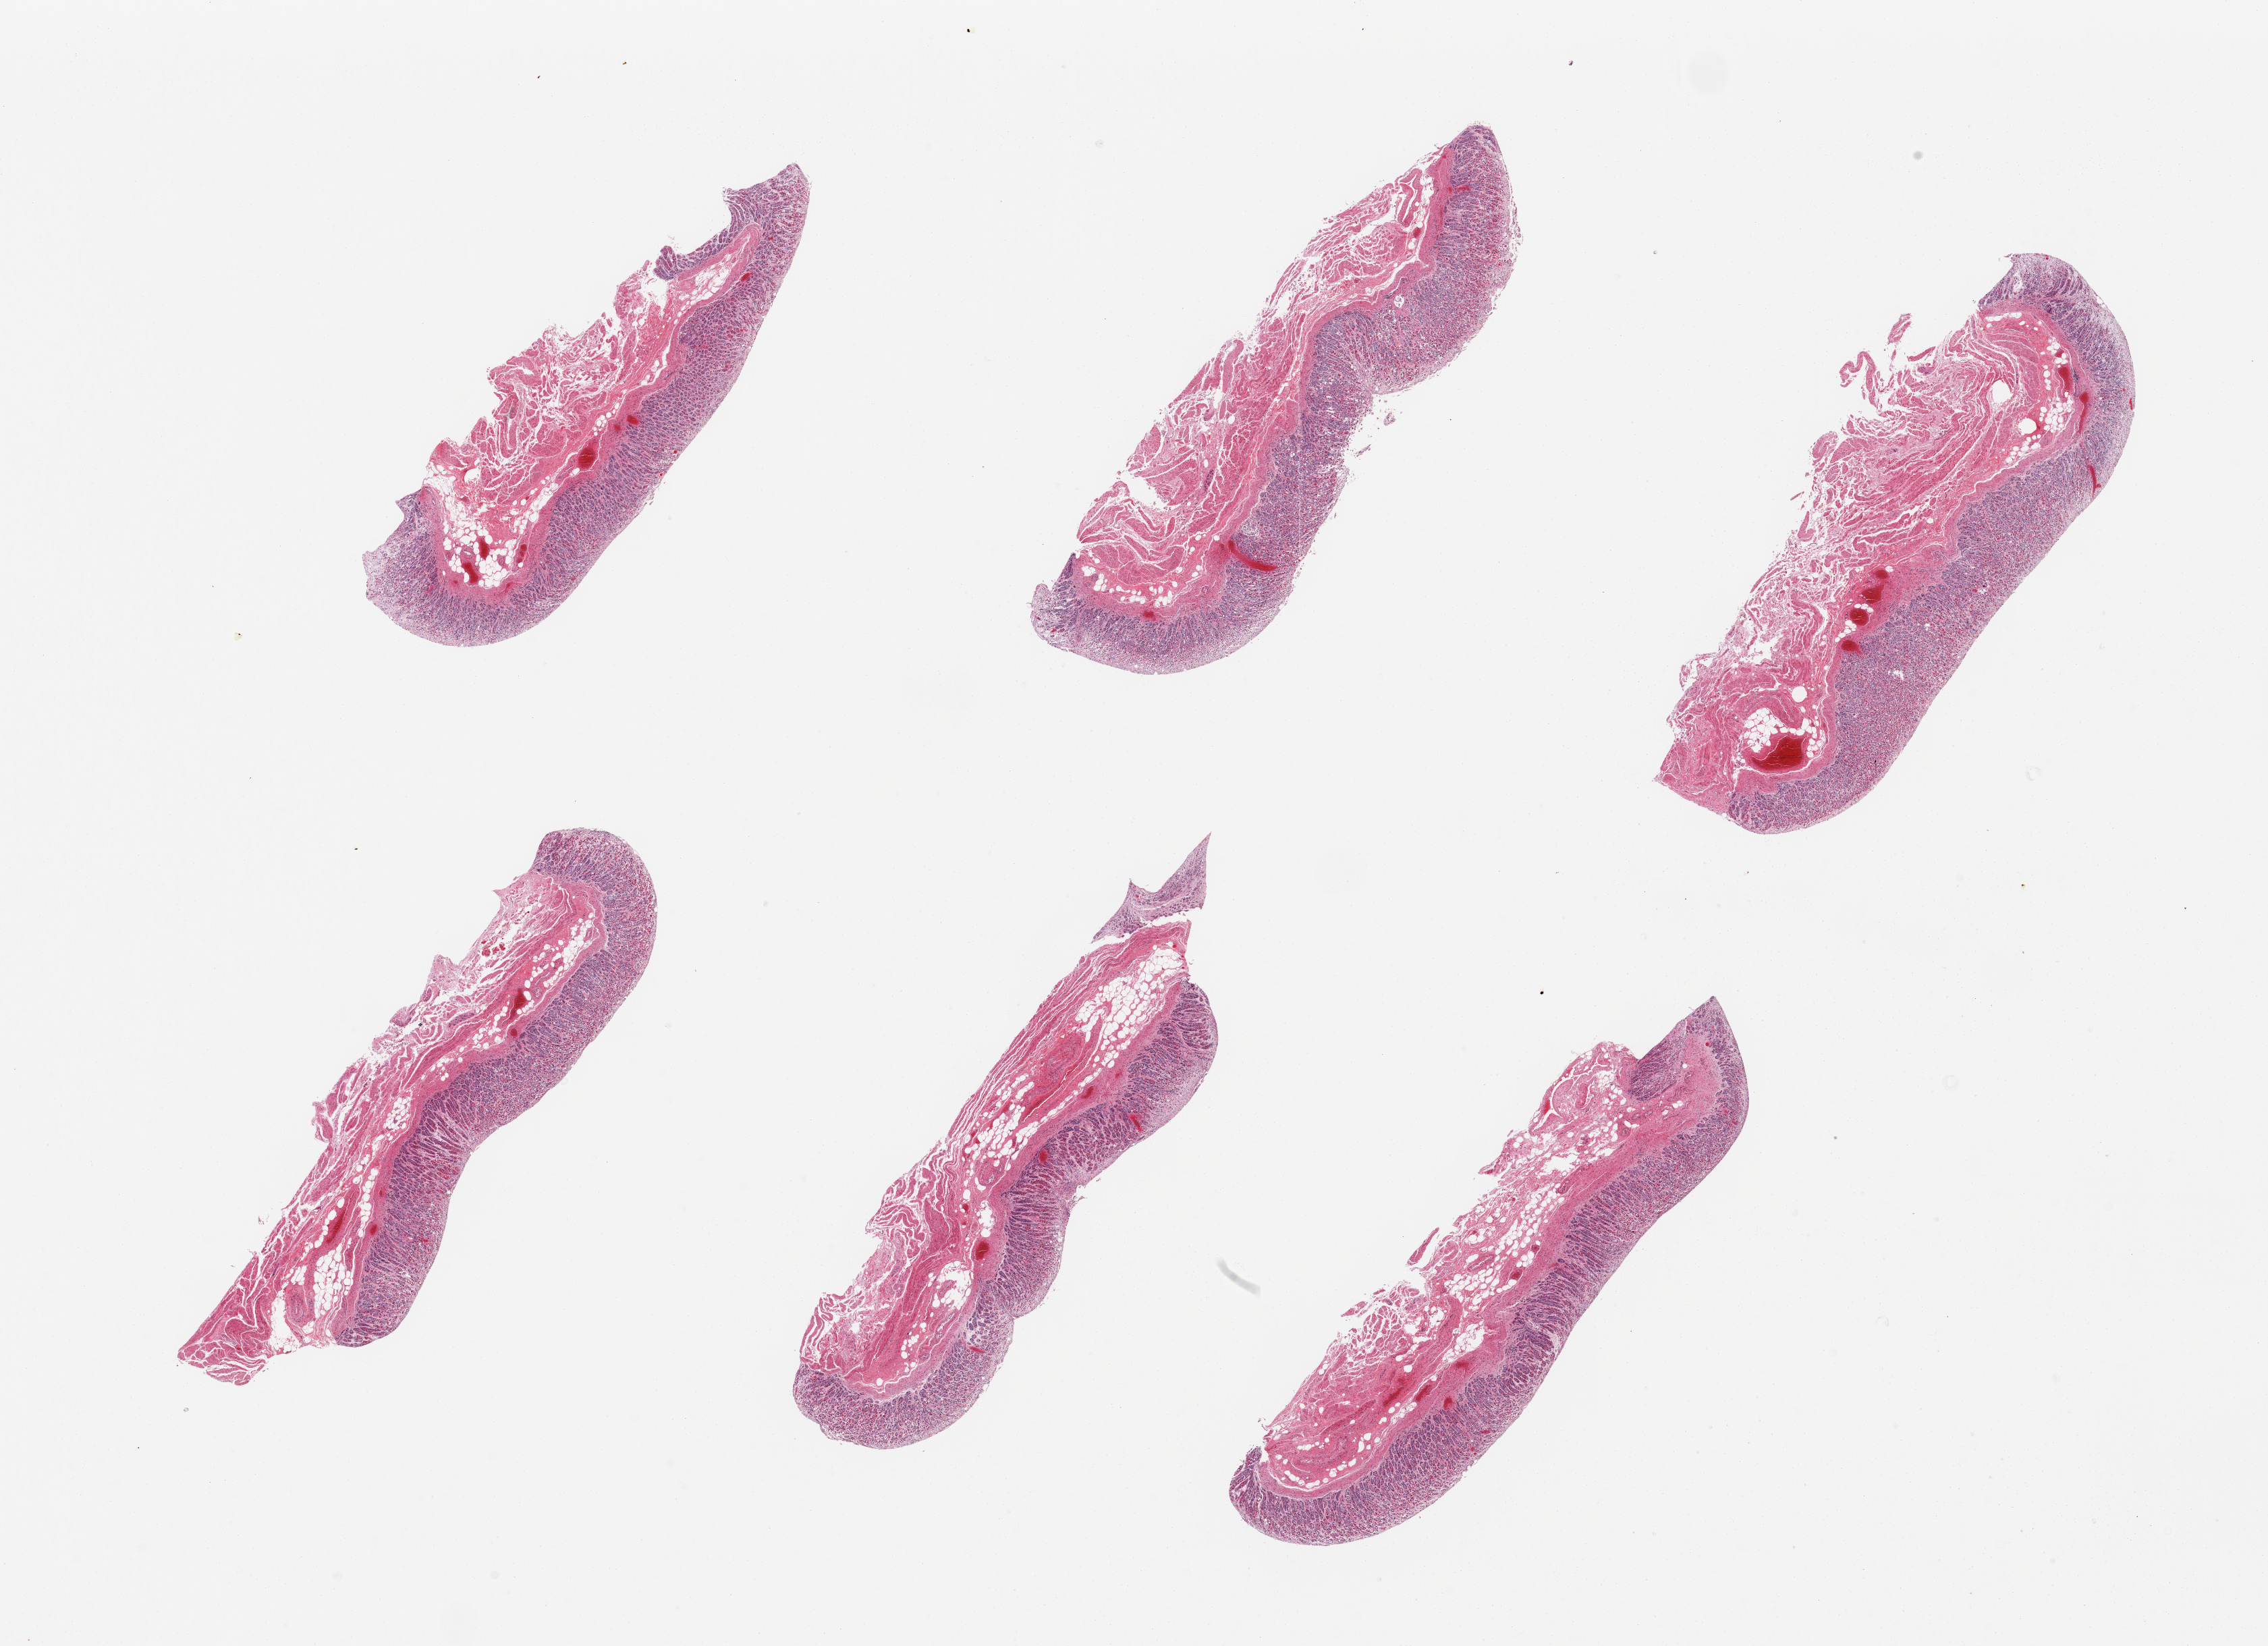
Haematoxylin and eosin whole-slide image, brightfield — whole scanned area (about 26.6 x 19.3 mm) shown as a low-resolution overview. PAXgene-fixed paraffin-embedded (PFPE) section. Sampled site (target tissue): stomach. Donor tissue sample. Donor: male.
Review note (as recorded): 6 pieces, mucosa up to ~1mm, ~40-50% thickness, but moderately-markedly autolyzed.